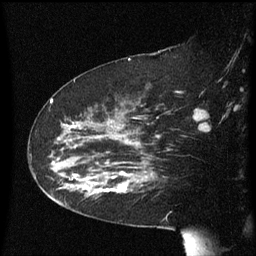
Breast MRI (dynamic contrast-enhanced), one sagittal slice. Dynamic contrast-enhanced series, image 2 of 3 at this slice position (ordered by acquisition). 1.5 T. TE 4.2 ms, TR 8.4 ms. 2.3 mm slice thickness. 256 × 256 image matrix, field of view 200 × 200 mm. Patient: female, 63 years. From the clinical record (not read from this slice): setting: breast cancer imaged before/during neoadjuvant chemotherapy; receptor status: HER2-positive.
Structures marked on this image (semi-automatic segmentation, software-assisted and operator-edited):
- analysis volume of interest (the breast-tissue region the enhancement analysis was run in; not a lesion): bounding box (x1, y1, x2, y2) in pixels: (71, 144, 147, 199)
- tumour enhancement mask (voxels above the 70 % enhancement threshold inside the analysis volume of interest): (94, 172, 147, 193)